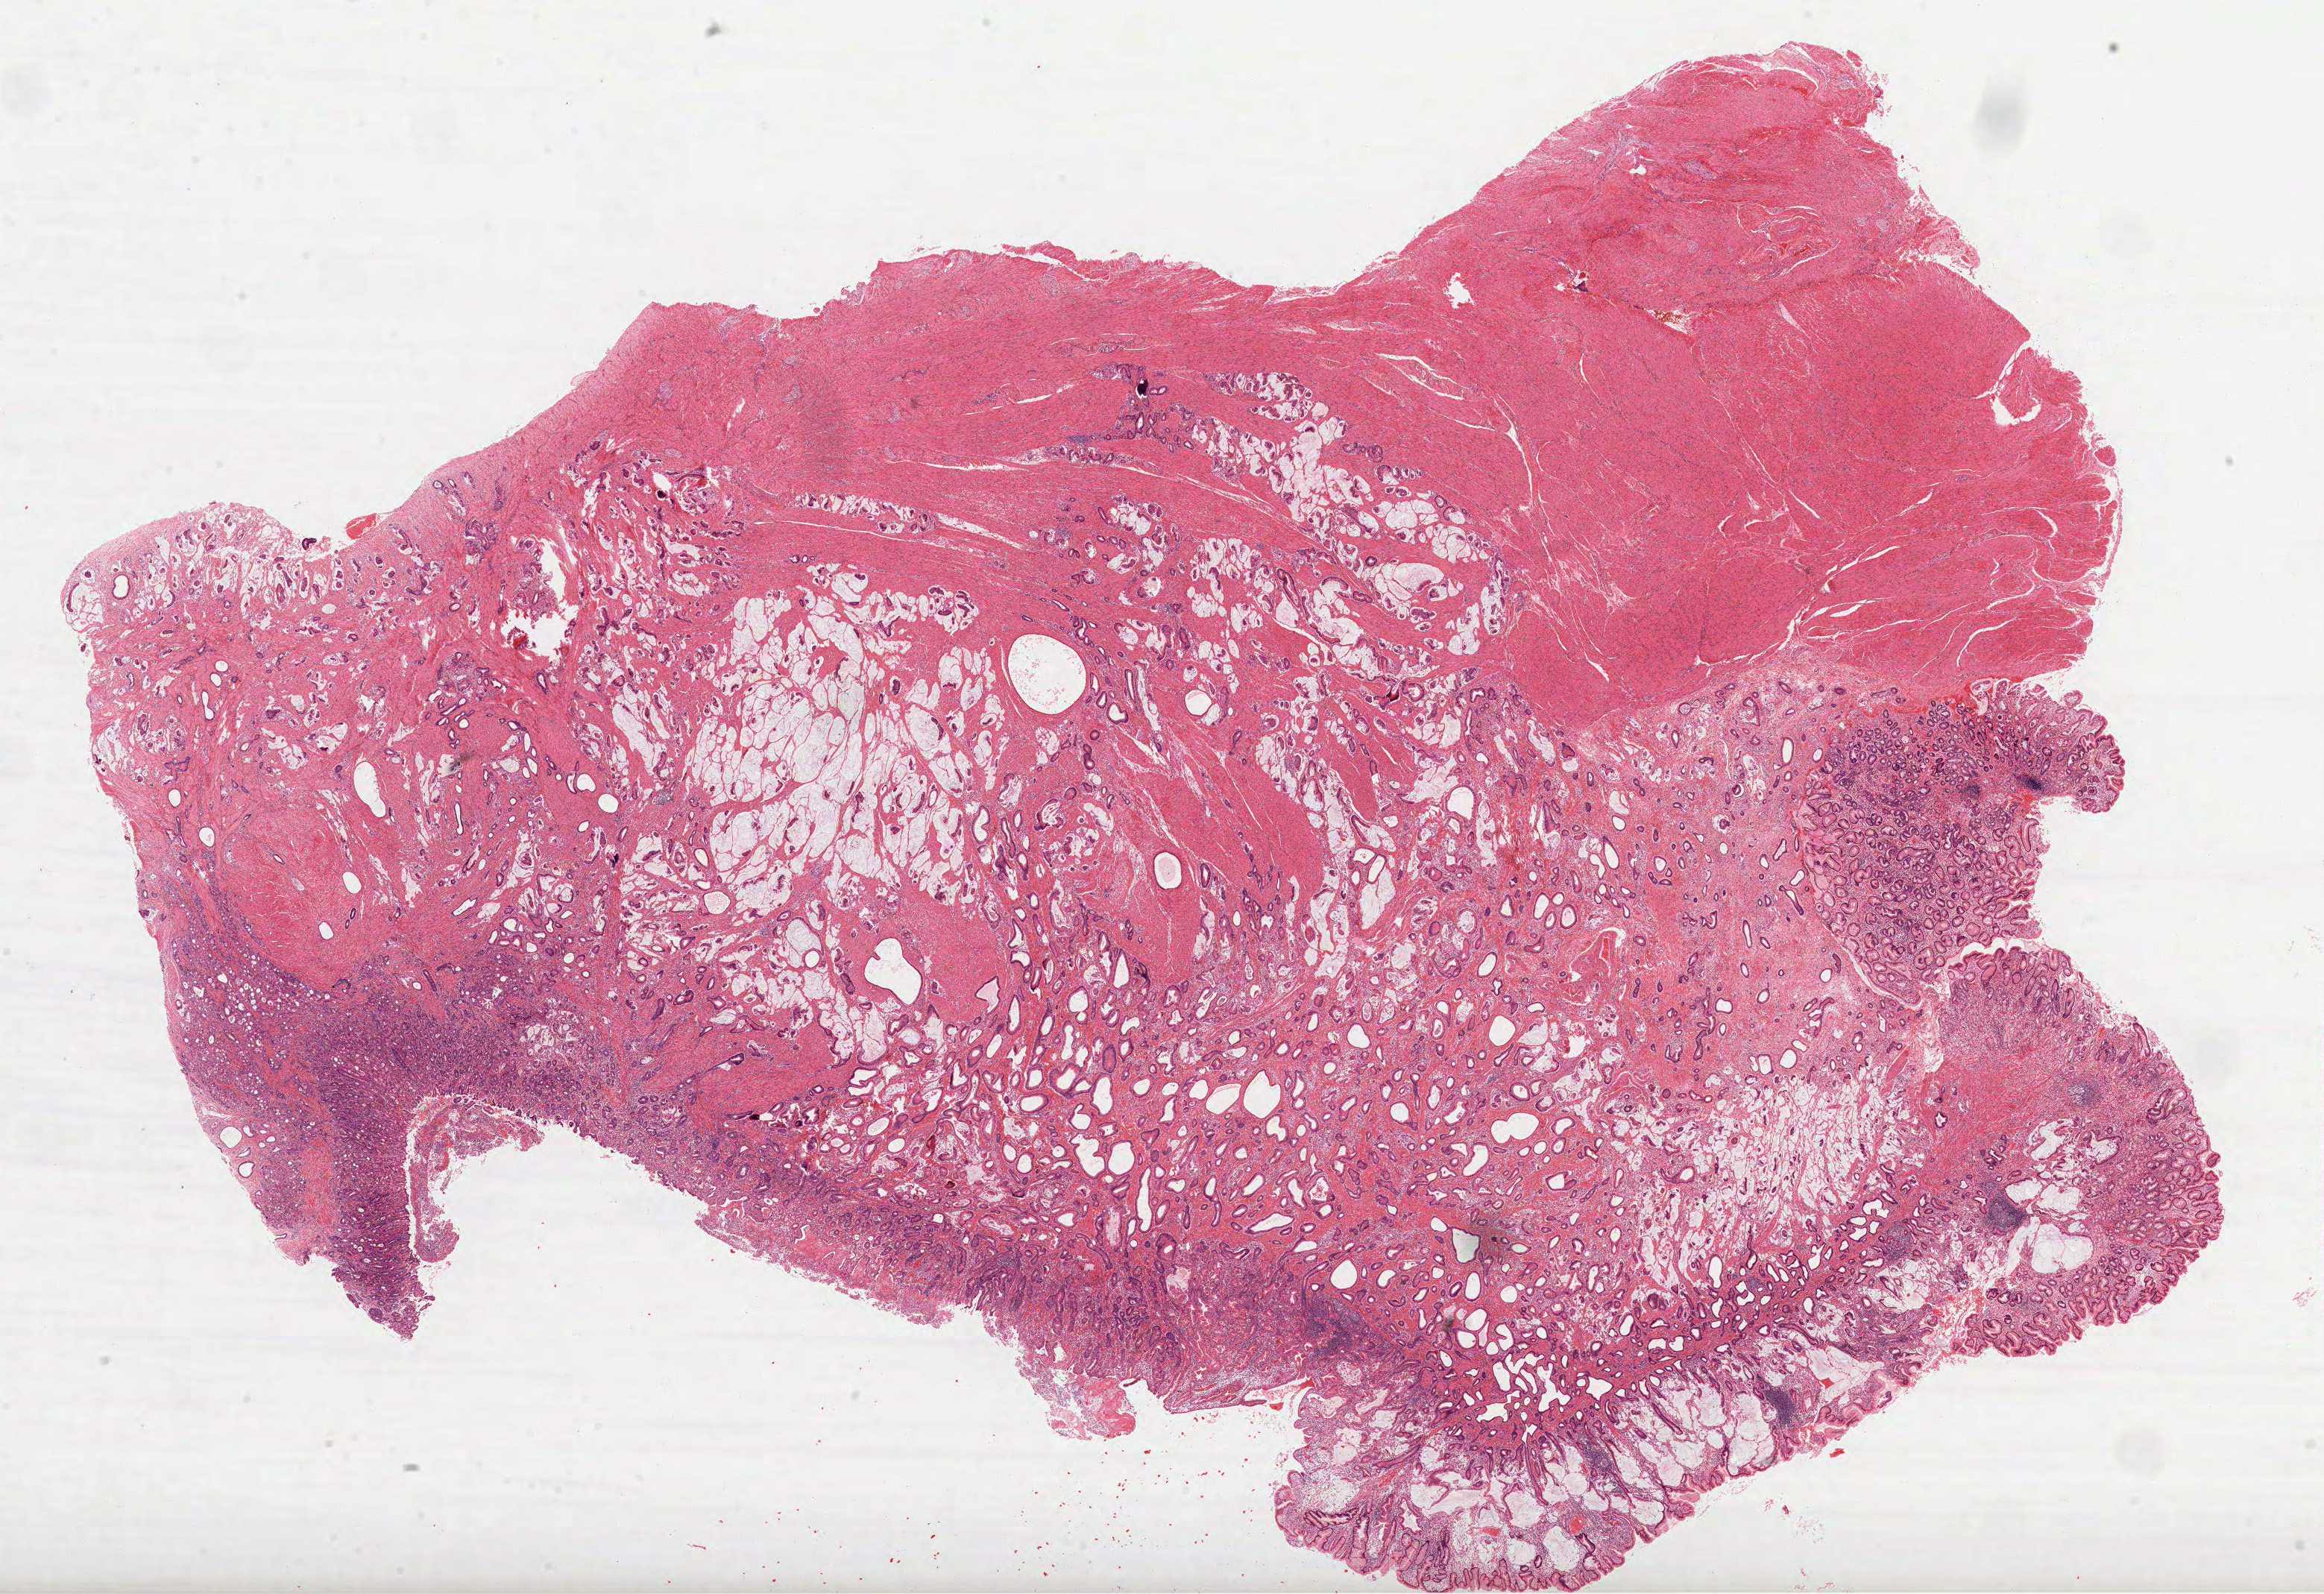
Whole-slide histology image, H&E — whole scanned area (about 25.1 x 17.2 mm) shown as a low-resolution overview; FFPE section; stomach, primary tumour sample. Patient: male, age at initial diagnosis 52 years. Histologic grade: G3 (poorly differentiated).
Lymph nodes positive (case pathology): 0 of 5 examined. Histologic diagnosis: Mucinous adenocarcinoma (gastric antrum). AJCC pathologic stage: IIB (7th edition). TNM: T4a N0 M0.